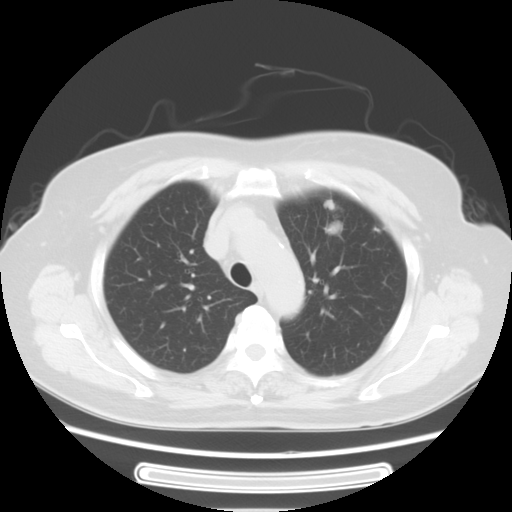
Chest CT, one axial slice. Slice 45 of 57 in the series (ordered by position). Reconstruction kernel STANDARD. Lung window (W 1500 / L -600 HU). 5 mm slice thickness. 512 × 512 image matrix, field of view 363 × 363 mm. Patient: female, 77 years. From the clinical record (not read from this slice): clinical TNM (as recorded): T1c N3 M0; histopathological grade: G2-3.
Structures marked on this image (rectangle marked by the reading radiologist):
- lung tumour (recorded histology: adenocarcinoma): bounding box [x1, y1, x2, y2] px = [317, 192, 366, 247]